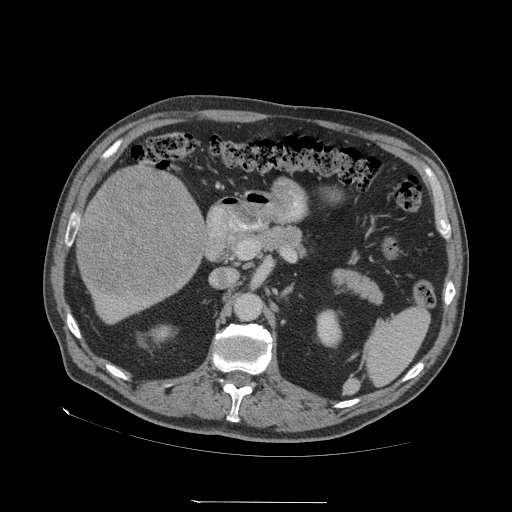
Contrast-enhanced abdominal CT (liver protocol), one axial slice. Slice 19 of 83 in the series (ordered by position). Reconstruction kernel STANDARD. Soft-tissue window (W 400 / L 40 HU). 2.5 mm slice thickness. 512 × 512 image matrix. From the clinical record (not read from this slice): diagnosis: hepatocellular carcinoma (patient treated with transarterial chemoembolisation; whether this scan precedes or follows treatment is not stated here); TNM stage (as recorded): Stage-I; Child-Pugh class: A; tumour differentiation: well differentiated; tumour nodularity: uninodular.
Annotated regions visible in this slice (semi-automatically segmented with operator editing):
- liver parenchyma outside the tumour (the mass and vessels are separate outlines, so this box may not span the whole liver): bounding box (x1, y1, x2, y2) in pixels: (76, 162, 208, 322)
- mass: (78, 168, 203, 297)